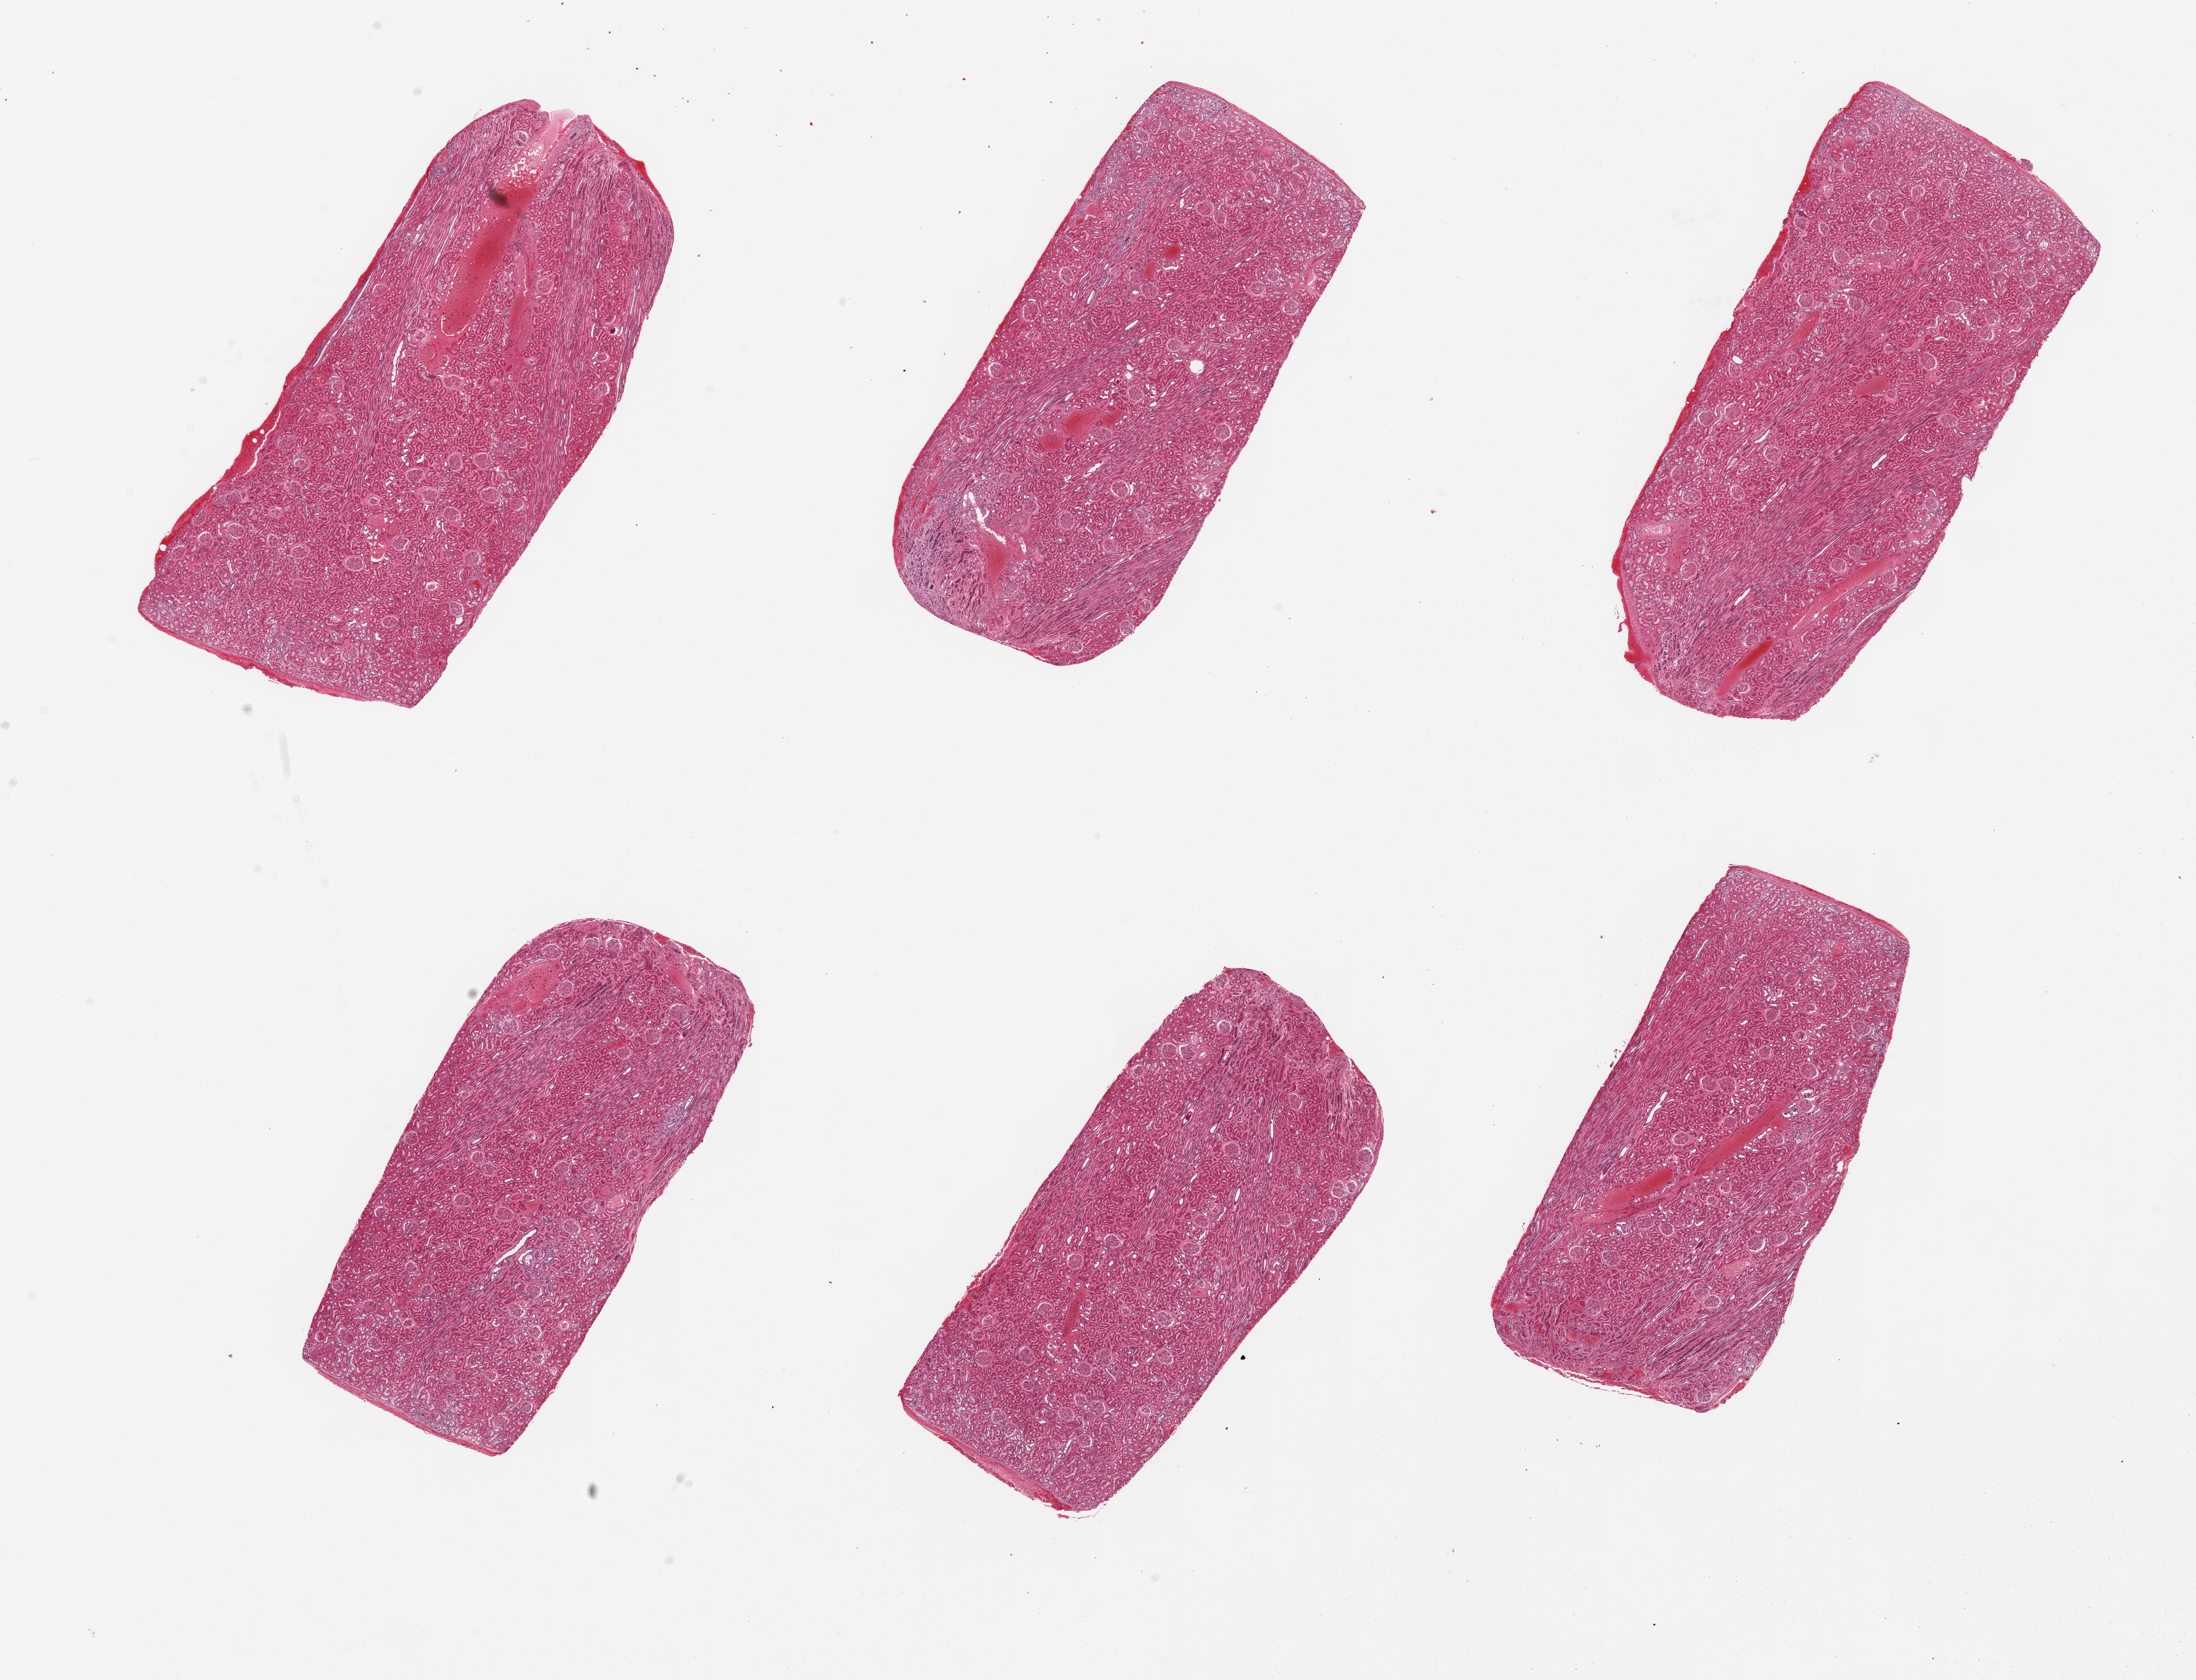
Haematoxylin and eosin whole-slide image, shown as a low-resolution overview of the whole scanned area (about 25.6 x 19.6 mm, from a 20x scan). PAXgene-fixed, paraffin-embedded tissue. Sampled site (target tissue): renal cortex. Donor tissue sample. Female donor.
Pathologist's review note for this sample: 6 pieces, glomeruli present in all sections.